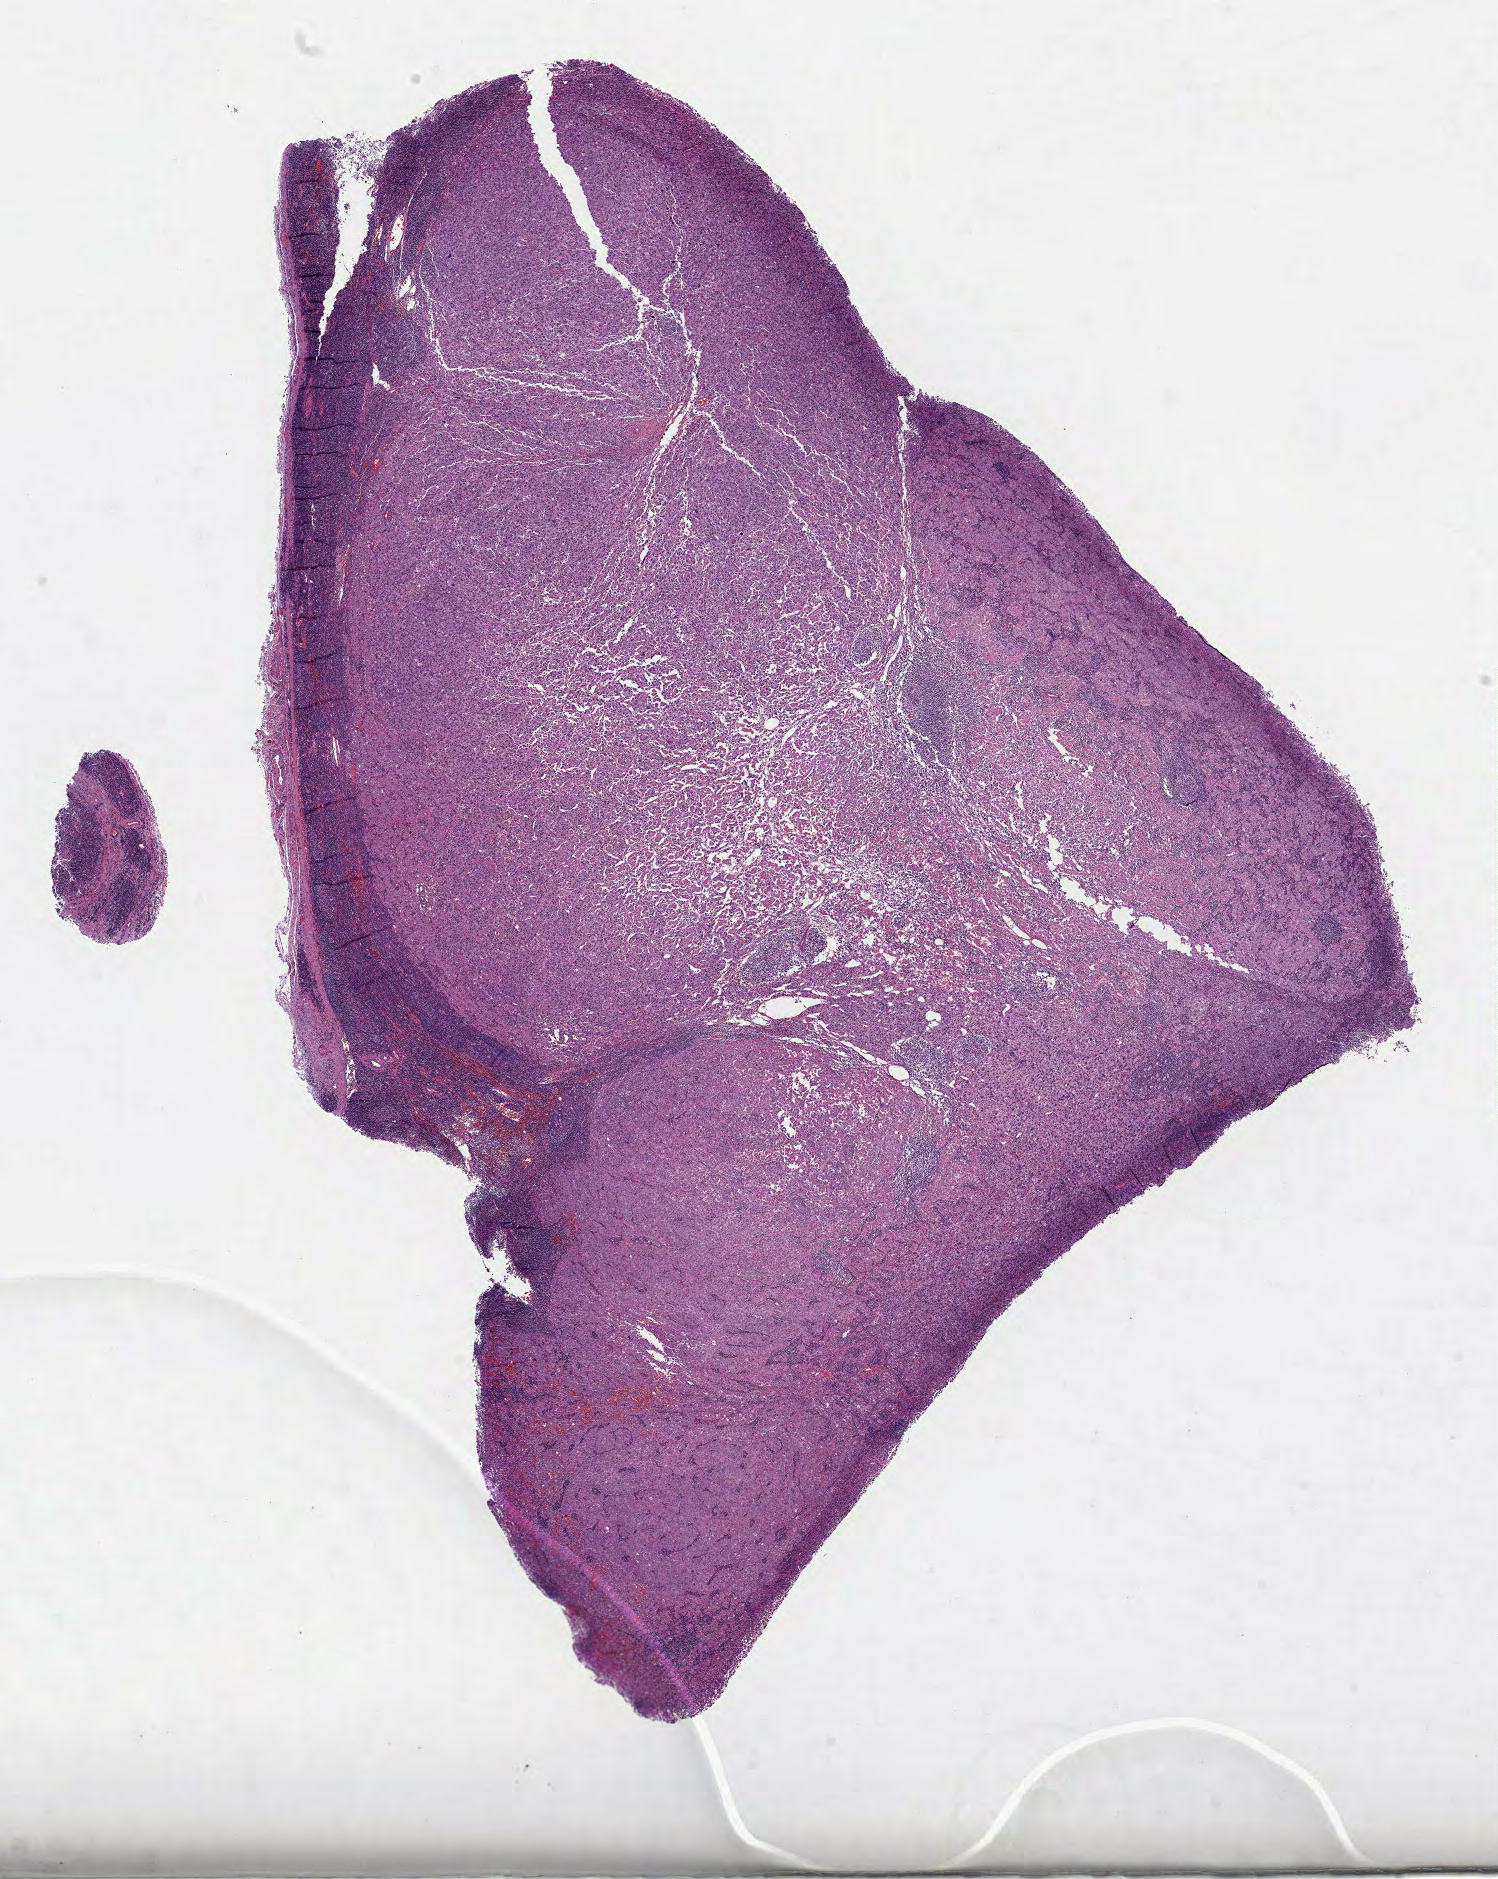
Whole-slide histology image, H&E, low-resolution overview of the scanned area, about 12.1 x 15.2 mm (acquisition: 40x scan), formalin-fixed paraffin-embedded (FFPE) diagnostic section, skin, primary tumour sample. Female, age 48 years at initial diagnosis.
Histologic diagnosis: Malignant melanoma, NOS.